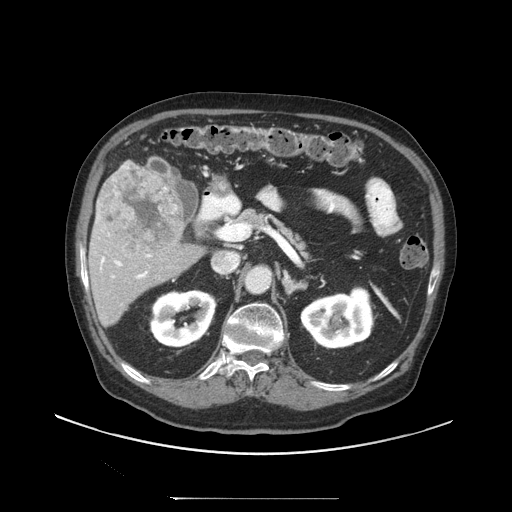
Contrast-enhanced abdominal CT (liver protocol), one axial slice. Position 51 of 97 along the scan axis. 140 kVp. Soft-tissue window (W 400 / L 40 HU). 2.5 mm slice thickness. 512 × 512 image matrix, field of view 450 × 450 mm. From the clinical record (not read from this slice): diagnosis: hepatocellular carcinoma (patient treated with transarterial chemoembolisation; whether this scan precedes or follows treatment is not stated here); TNM stage (as recorded): Stage-IIIC; Child-Pugh class: A; tumour differentiation: well differentiated; tumour size: 9.2 cm.
Structures marked on this image (semi-automatically segmented with operator editing):
- liver parenchyma outside the tumour (the mass and vessels are separate outlines, so this box may not span the whole liver): box from (x=88, y=160) to (x=204, y=326) px
- mass: (x=99, y=166)–(x=184, y=259)
- liver vessels: (x=96, y=165)–(x=147, y=279)